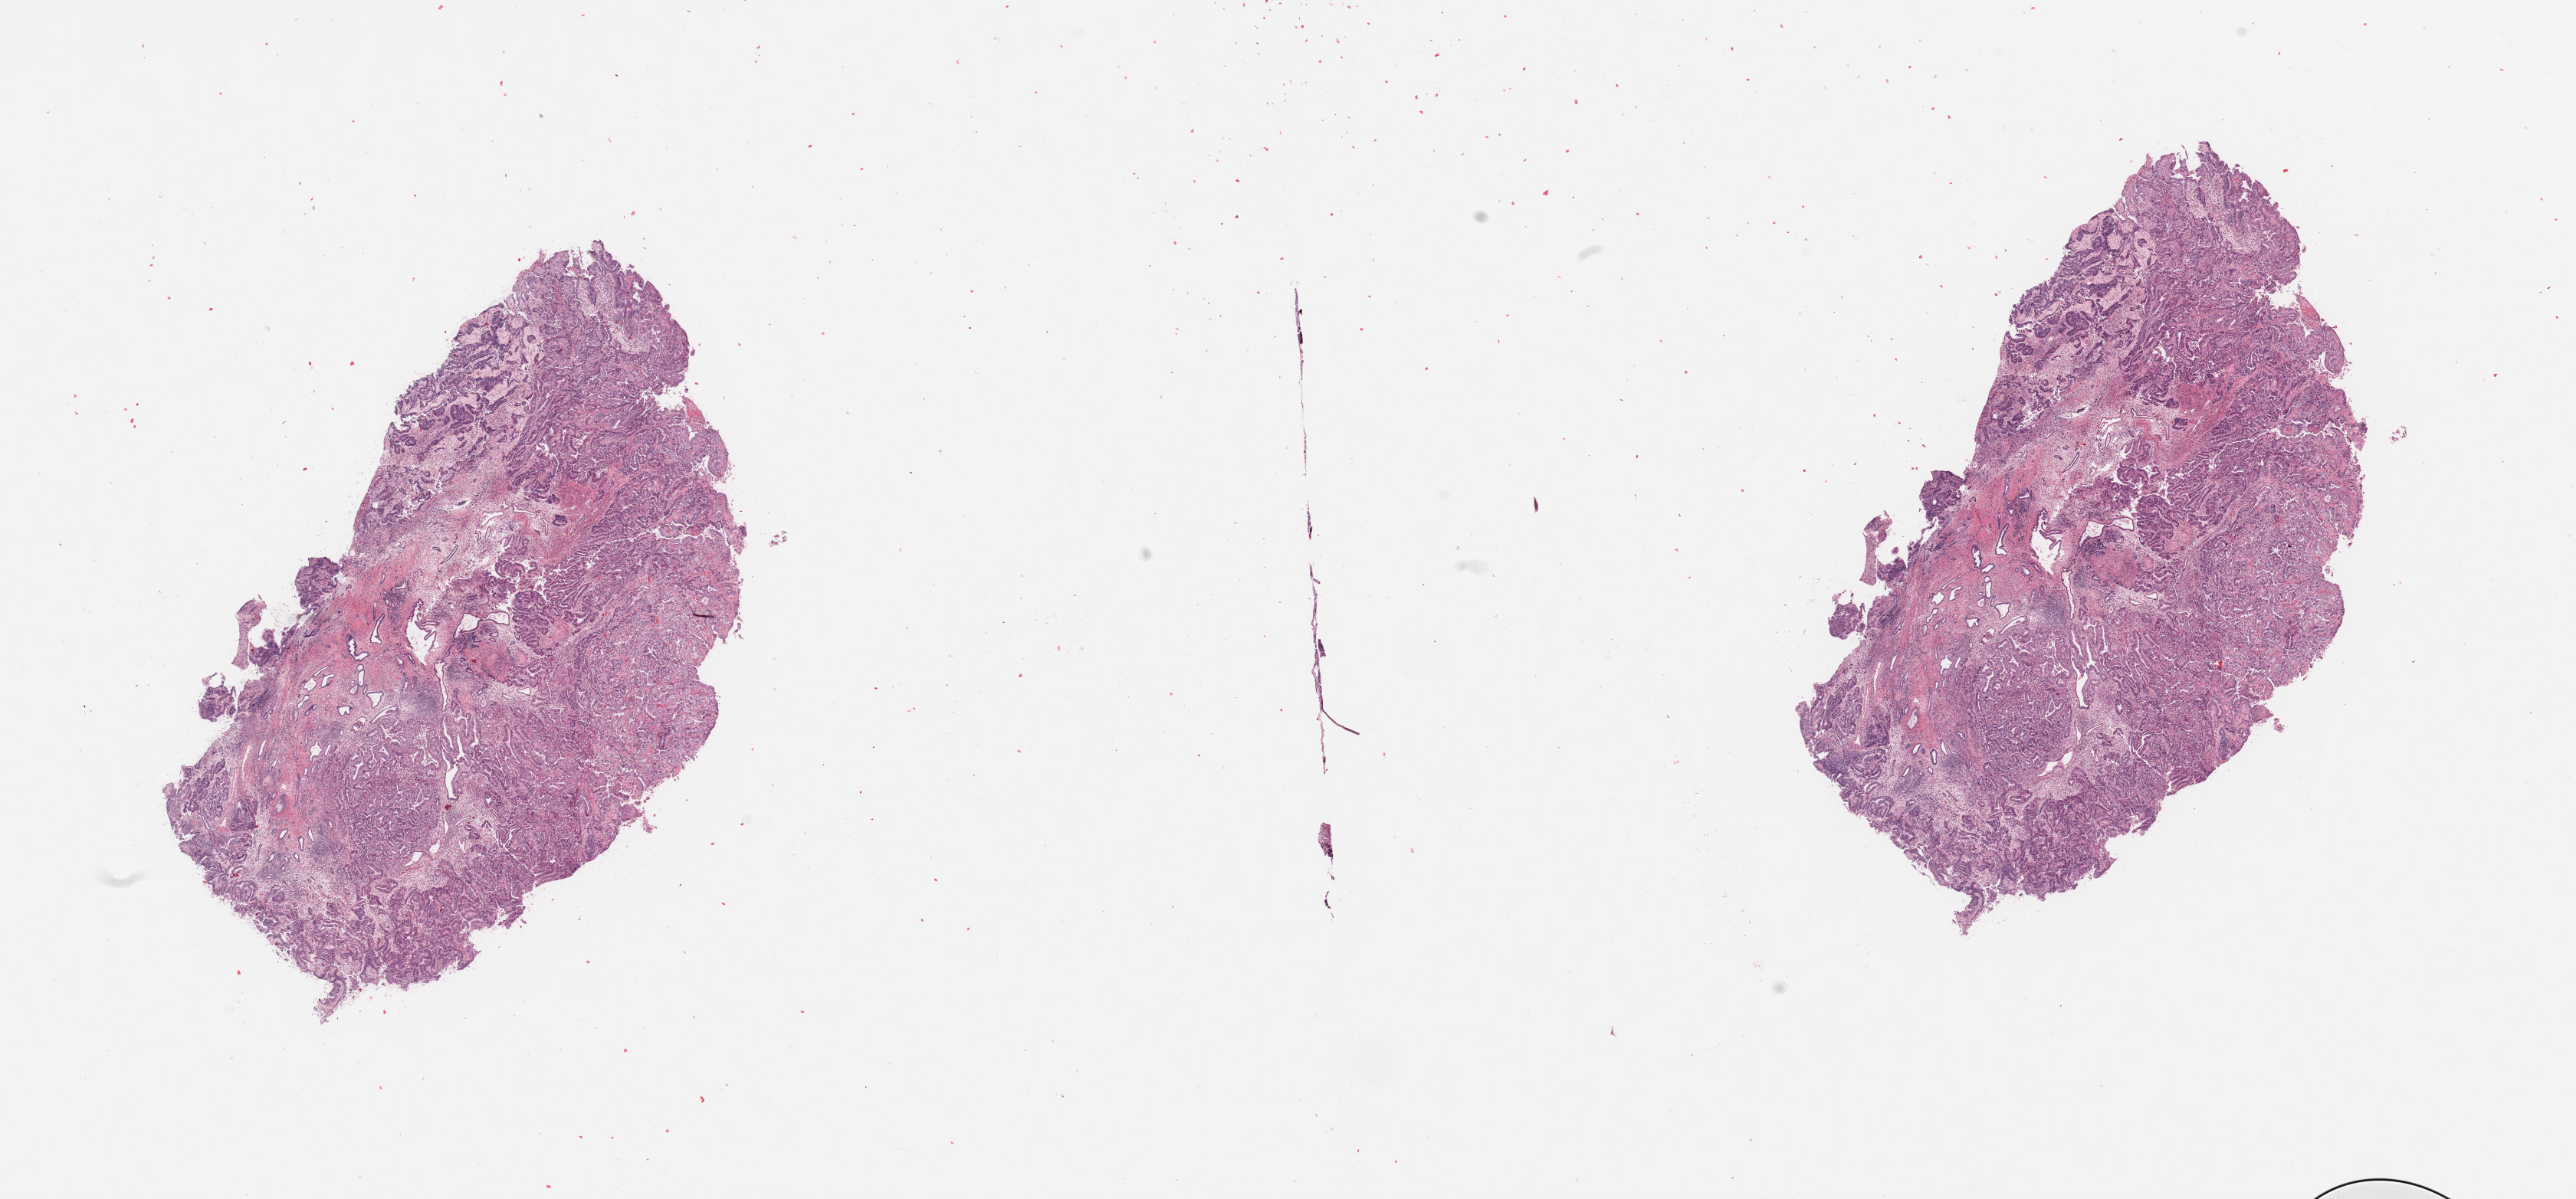
Whole-slide histology image, Hematoxylin and eosin (H&E) stained — a low-resolution overview of the entire scanned area, about 26.6 x 12.4 mm, tumour tissue sample, sampled site: uterus. Female, 86 y/o. Histologic grade: G2 (moderately differentiated). Pathologist review of this section (percent, as recorded): tumour nuclei 80%, necrosis 0%.
AJCC pathologic stage: IB. Diagnosis: Endometrioid adenocarcinoma, NOS.